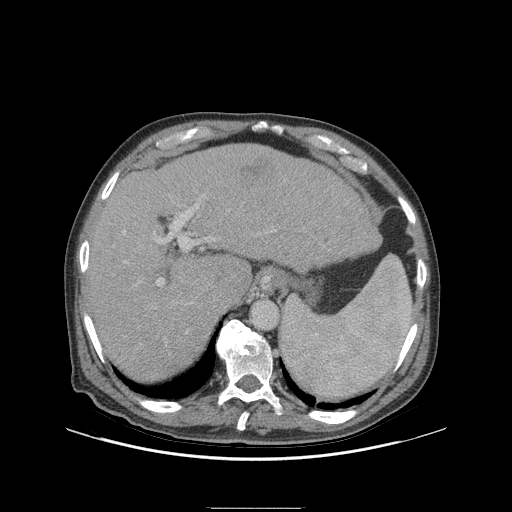
Contrast-enhanced abdominal CT (liver protocol), one axial slice; position 72 of 105 along the scan axis; reconstruction kernel STANDARD; soft-tissue window (W 400 / L 40 HU); 512 × 512 image matrix. From the clinical record (not read from this slice): diagnosis: hepatocellular carcinoma (patient treated with transarterial chemoembolisation; whether this scan precedes or follows treatment is not stated here); TNM stage (as recorded): Stage-I; Child-Pugh class: A; tumour nodularity: uninodular.
Outlined on this slice (semi-automatically segmented with operator editing):
- liver parenchyma outside the tumour (the mass and vessels are separate outlines, so this box may not span the whole liver): bounding box <86,144,380,380> (left, top, right, bottom; pixels)
- mass: <240,162,263,185>
- liver vessels: <123,195,273,286>